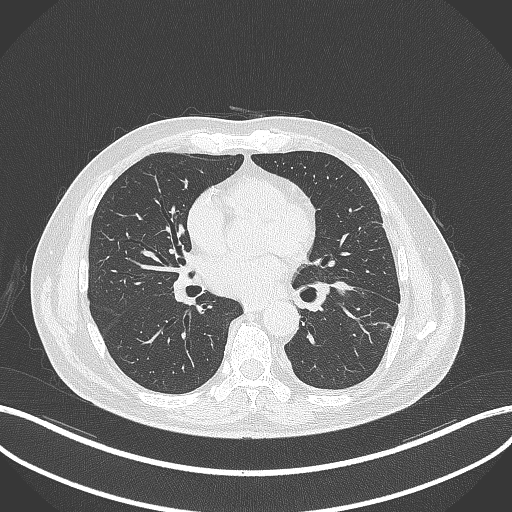
Chest CT, one axial slice; slice 174 of 230 in the series (ordered by position); reconstruction kernel B70f; lung window (W 1500 / L -600 HU); 1 mm slice thickness; 512 × 512 image matrix. Patient: male, 68 years. From the clinical record (not read from this slice): clinical TNM (as recorded): T2b N0 M0.
Outlined on this slice (bounding box drawn by a radiologist):
- lung tumour (recorded histology: squamous cell carcinoma): bounding box <326,272,358,296> (left, top, right, bottom; pixels)